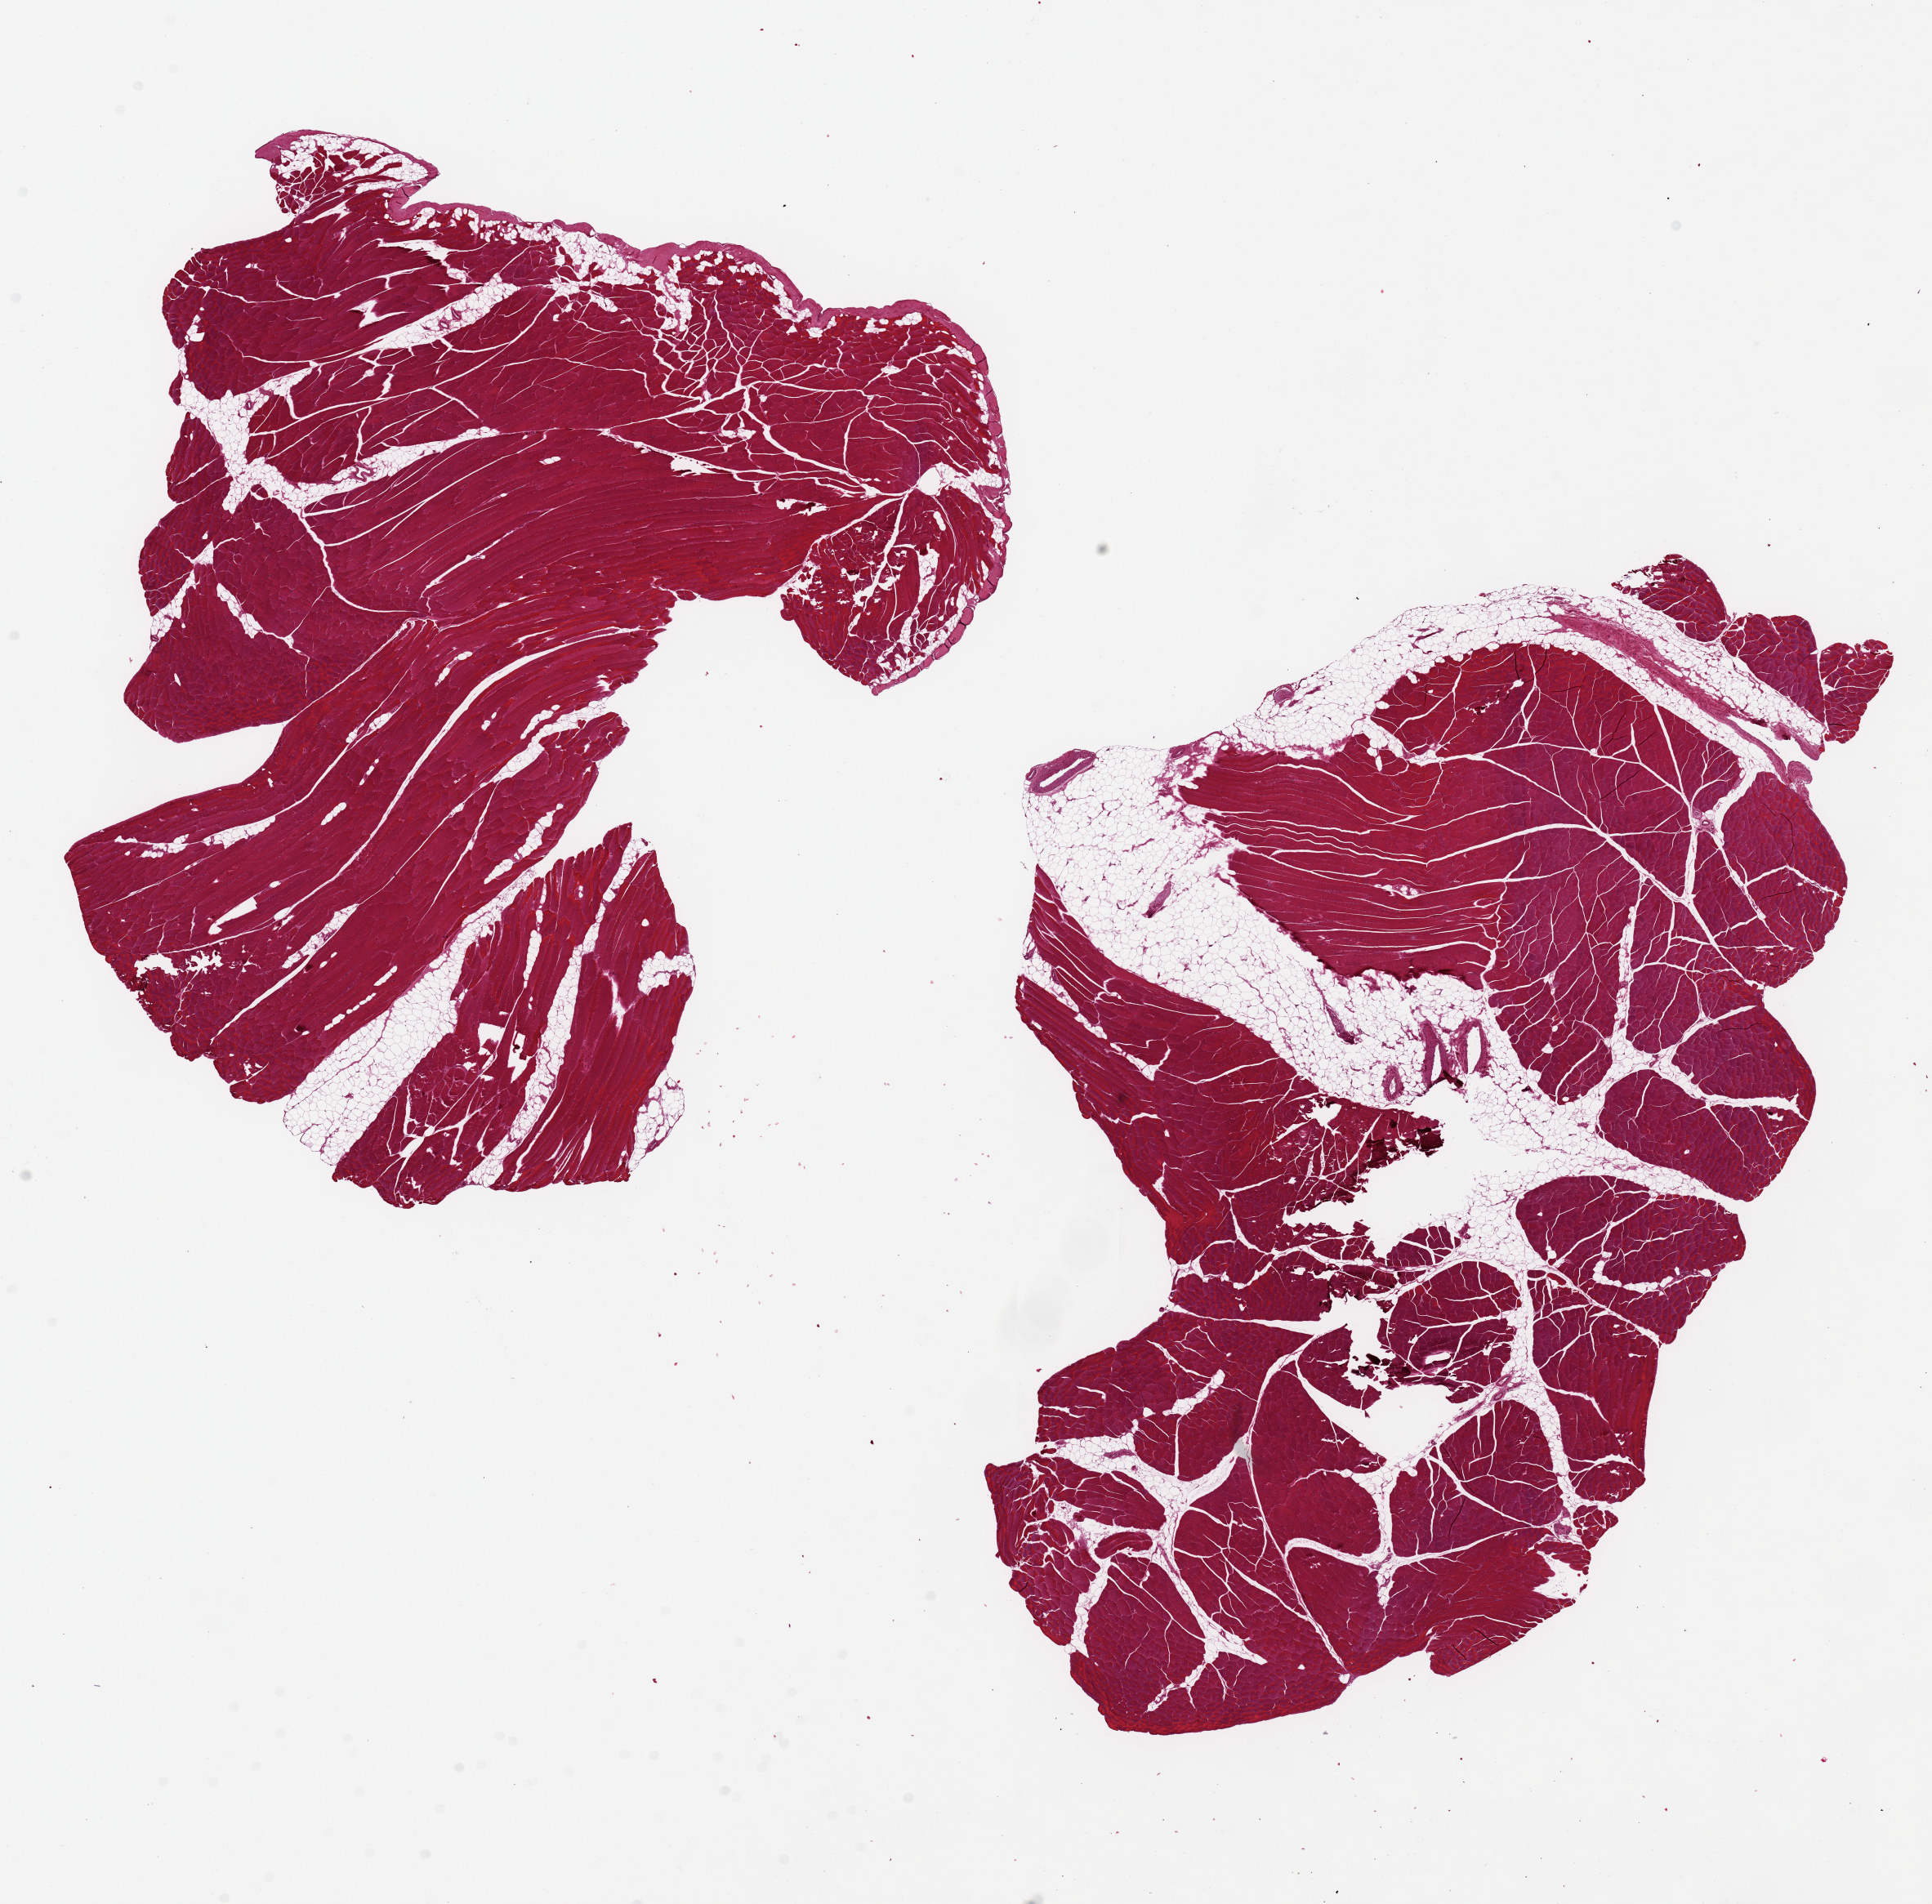
Whole-slide image, H&E stain, brightfield — a low-resolution overview of the entire scanned area, about 18.7 x 18.4 mm, PAXgene-fixed, paraffin-embedded tissue, target tissue: skeletal muscle, tissue donor sample. Donor sex: male.
Reviewer comment on this tissue sample: 2 pieces, 11x9 7 13x8.5mm; ~ 10% interstital fat.